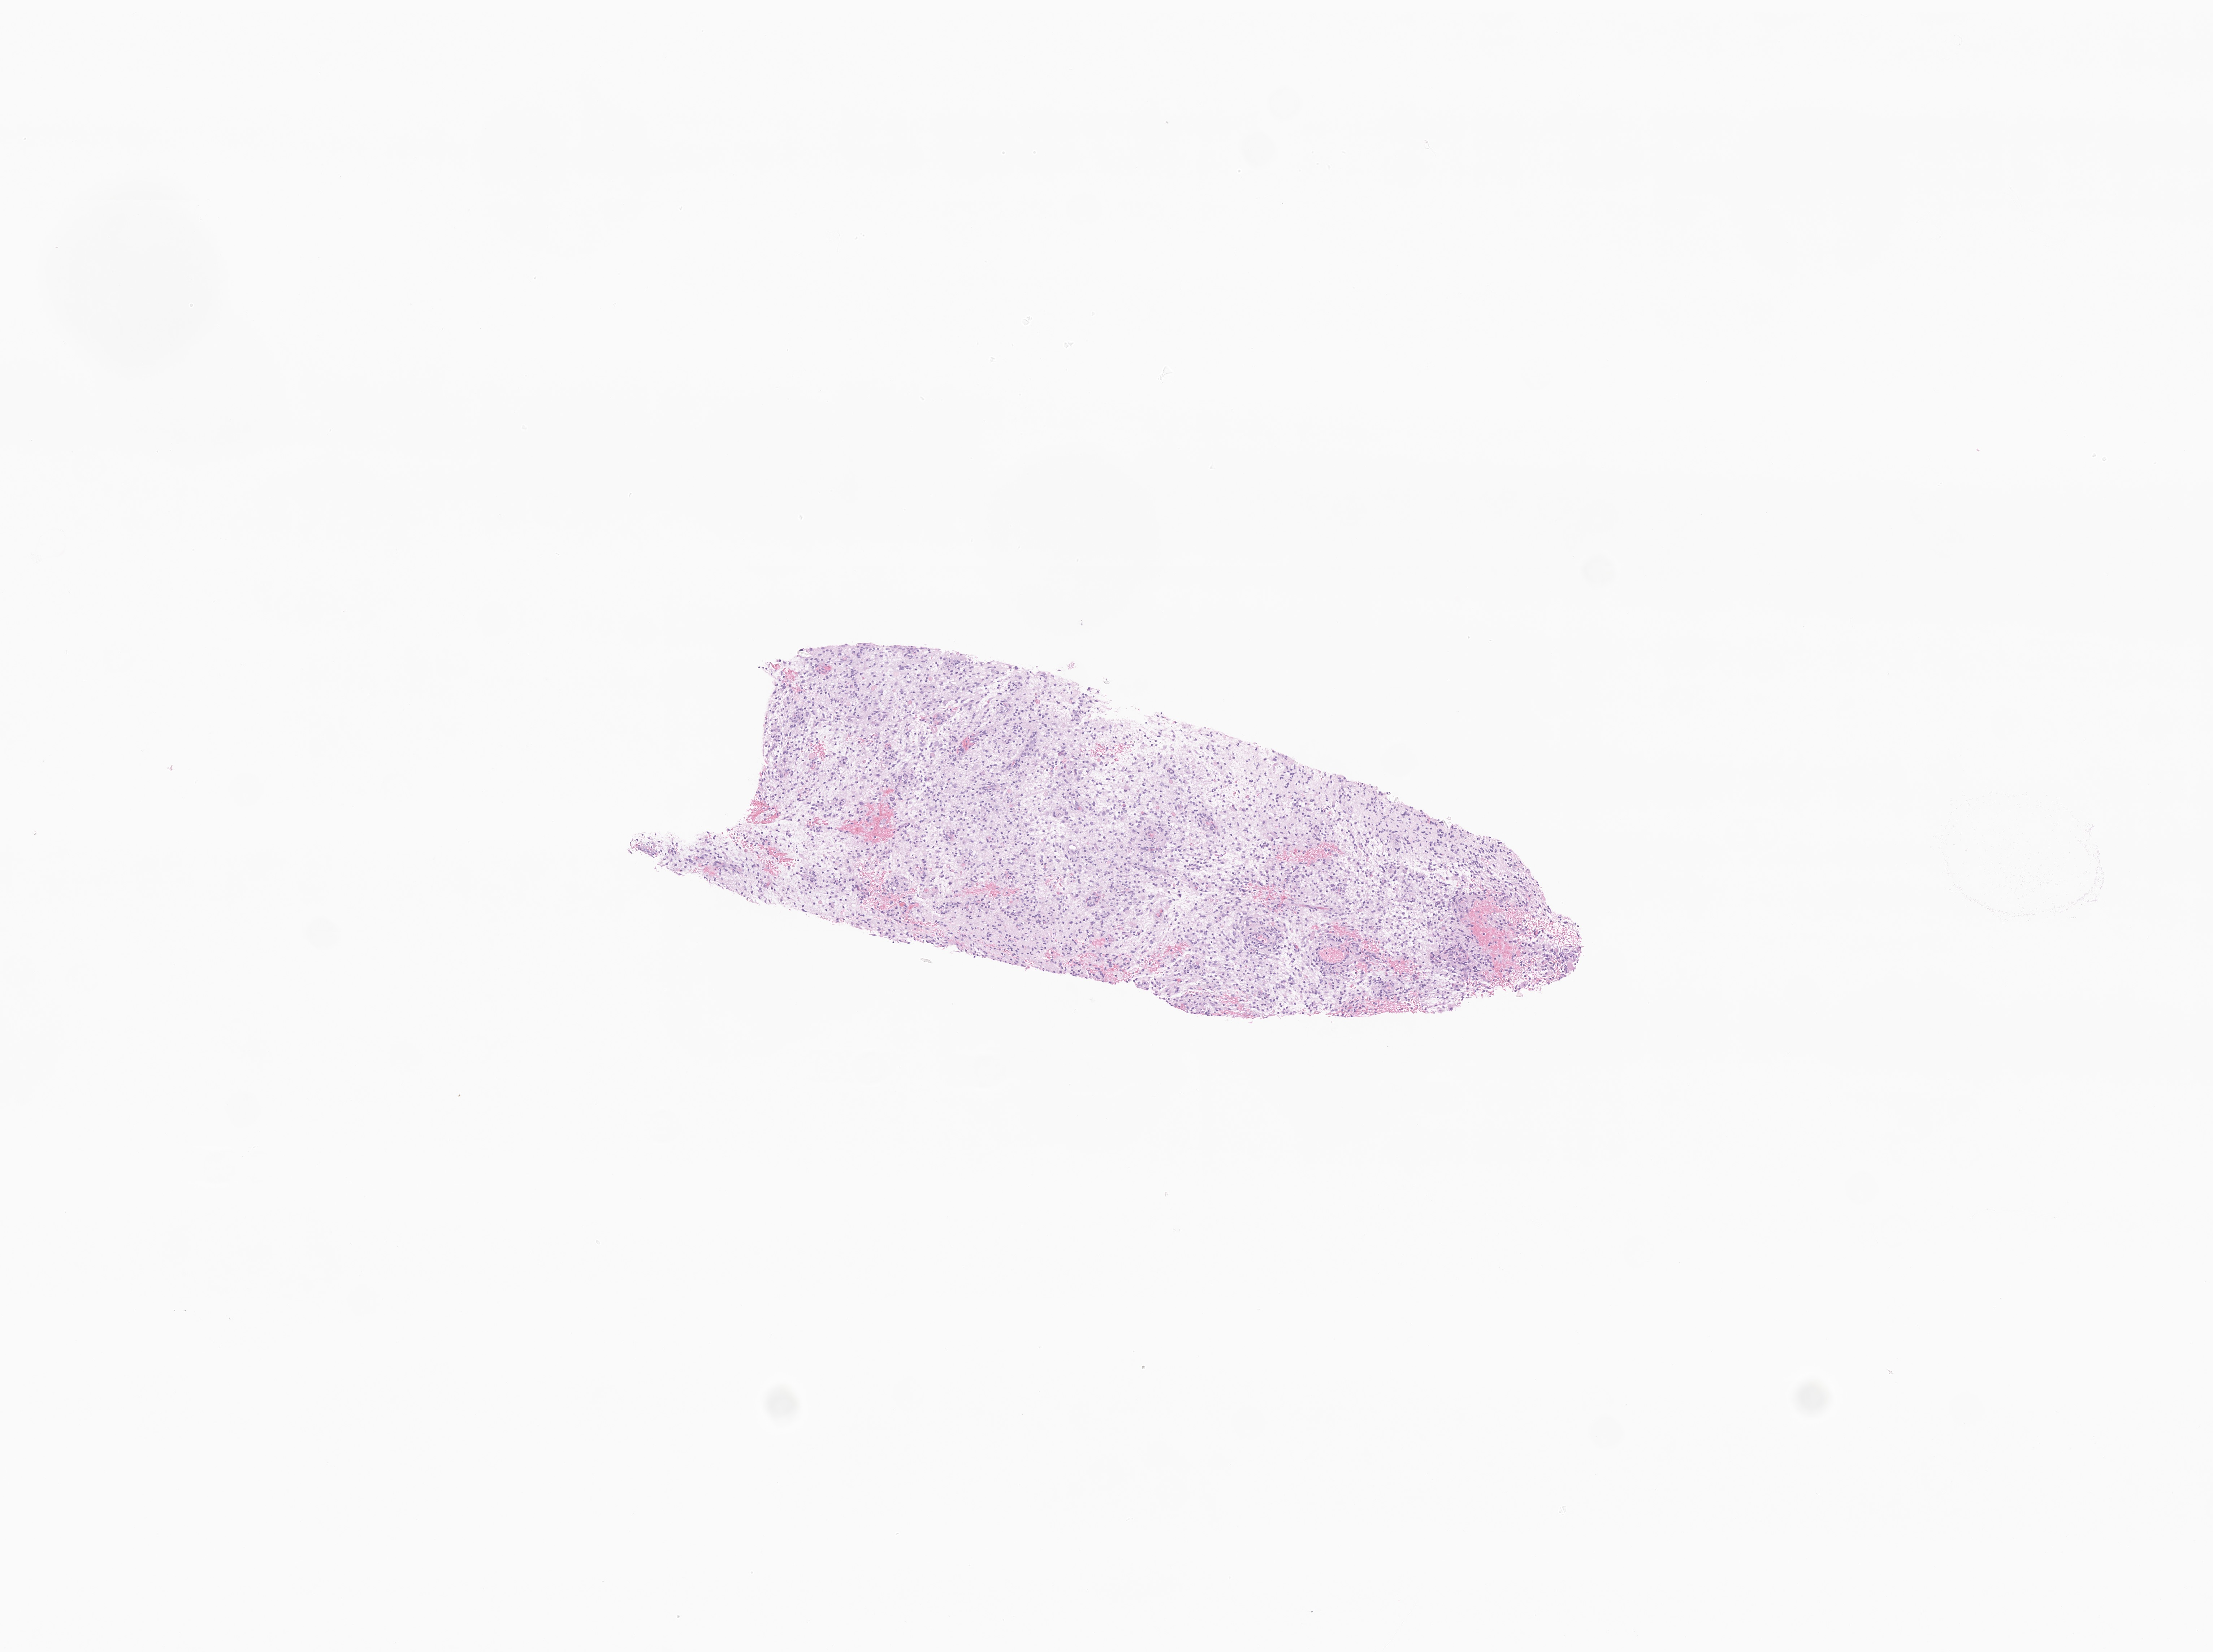
Whole-slide image, haematoxylin and eosin stain of tumor tissue from the brain, shown as a low-resolution overview of the whole scanned area (about 6.5 x 4.8 mm); formalin-fixed paraffin-embedded section. Patient: female, age 36 months (3 years).
- recorded diagnosis: Neoplasm, uncertain whether benign or malignant